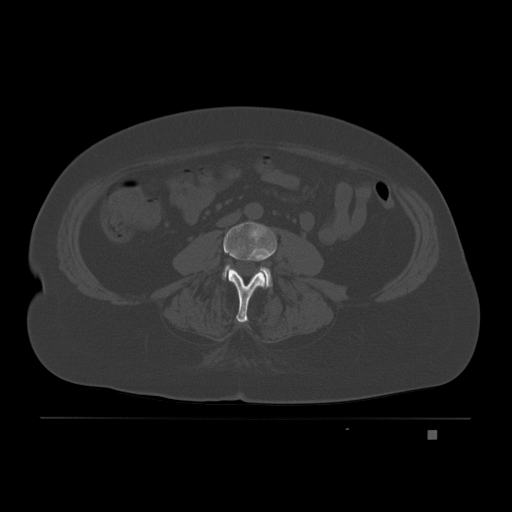
CT including the spine, one axial slice. Slice 48 of 221 in the series (ordered by position). Bone window (W 1800 / L 400 HU). 3 mm slice thickness. 512 × 512 image matrix, field of view 474 × 474 mm. Patient: female, 63 years. From the clinical record (not read from this slice): primary cancer: breast.
Outlined on this slice (semi-automatically segmented with operator editing):
- L3 vertebra: bounding box <223,222,277,323> (left, top, right, bottom; pixels)
- L4 vertebra: <222,264,272,288>